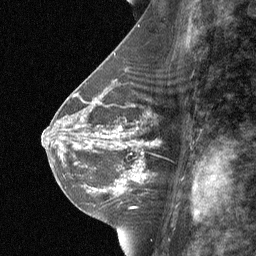
Breast MRI (dynamic contrast-enhanced), one sagittal slice. Slice 34 of 64 in the series (ordered by position). Dynamic contrast-enhanced study with each time point stored as its own series, time point 2 of 3 at this slice position (early post-contrast, ordered by acquisition time). 1.5 T. TE 4.8 ms, TR 27 ms. 2 mm slice thickness. 256 × 256 image matrix. Female patient, age 42 years. Case-level facts recorded for this patient, not image findings: setting: breast cancer imaged before/during neoadjuvant chemotherapy; receptor status: triple-negative.
Annotated regions visible in this slice (semi-automatic segmentation, software-assisted and operator-edited):
- analysis volume of interest (the breast-tissue region the enhancement analysis was run in; not a lesion): bounding box (x1, y1, x2, y2) in pixels: (99, 117, 172, 187)
- tumour enhancement mask (voxels above the 90 % enhancement threshold inside the analysis volume of interest): (117, 126, 157, 187)